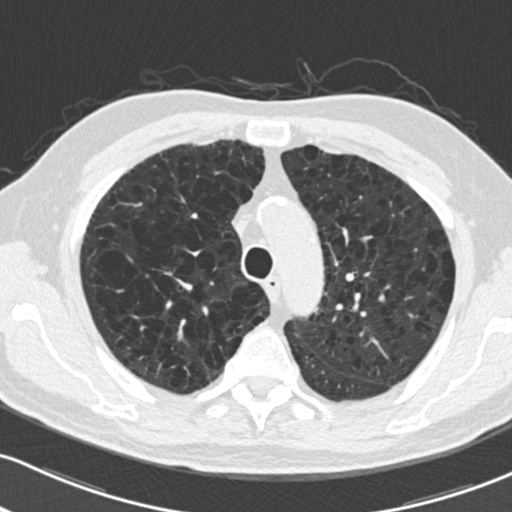
Low-dose screening chest CT, one axial slice; slice 157 of 204 in the series (ordered by position); 120 kVp; lung window (W 1500 / L -600 HU); 2 mm slice thickness; 512 × 512 image matrix.
Structures marked on this image (outlined manually by an expert reader):
- lesion 1 (tumor, upper lobe of right lung): bounding box [x1, y1, x2, y2] px = [164, 272, 172, 276]